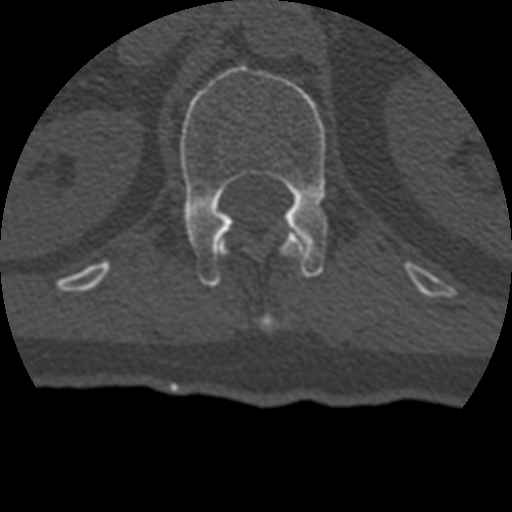
CT including the spine, one axial slice. Position 155 of 399 along the scan axis. 120 kVp. Bone window (W 1800 / L 400 HU). 1.25 mm slice thickness. 512 × 512 image matrix, field of view 160 × 160 mm. Patient age 69 years. Case-level facts recorded for this patient, not image findings: primary cancer: prostate.
Outlined on this slice (semi-automatically segmented with operator editing):
- L1 vertebra: bounding box [x1, y1, x2, y2] px = [180, 64, 328, 286]
- T12 vertebra: [223, 231, 307, 329]